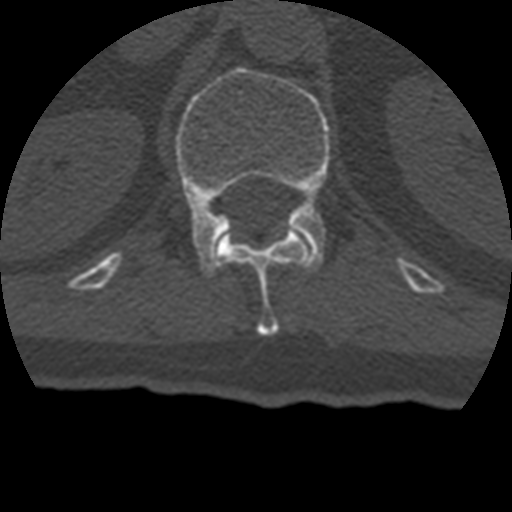
CT including the spine, one axial slice; position 158 of 399 along the scan axis; reconstruction kernel STANDARD; 120 kVp; bone window (W 1800 / L 400 HU); 1.25 mm slice thickness; 512 × 512 image matrix. Patient age 69 years. Case-level facts recorded for this patient, not image findings: primary cancer: prostate.
Structures marked on this image (semi-automatically segmented with operator editing):
- L1 vertebra: bounding box <175,66,330,276> (left, top, right, bottom; pixels)
- T12 vertebra: <215,226,311,336>